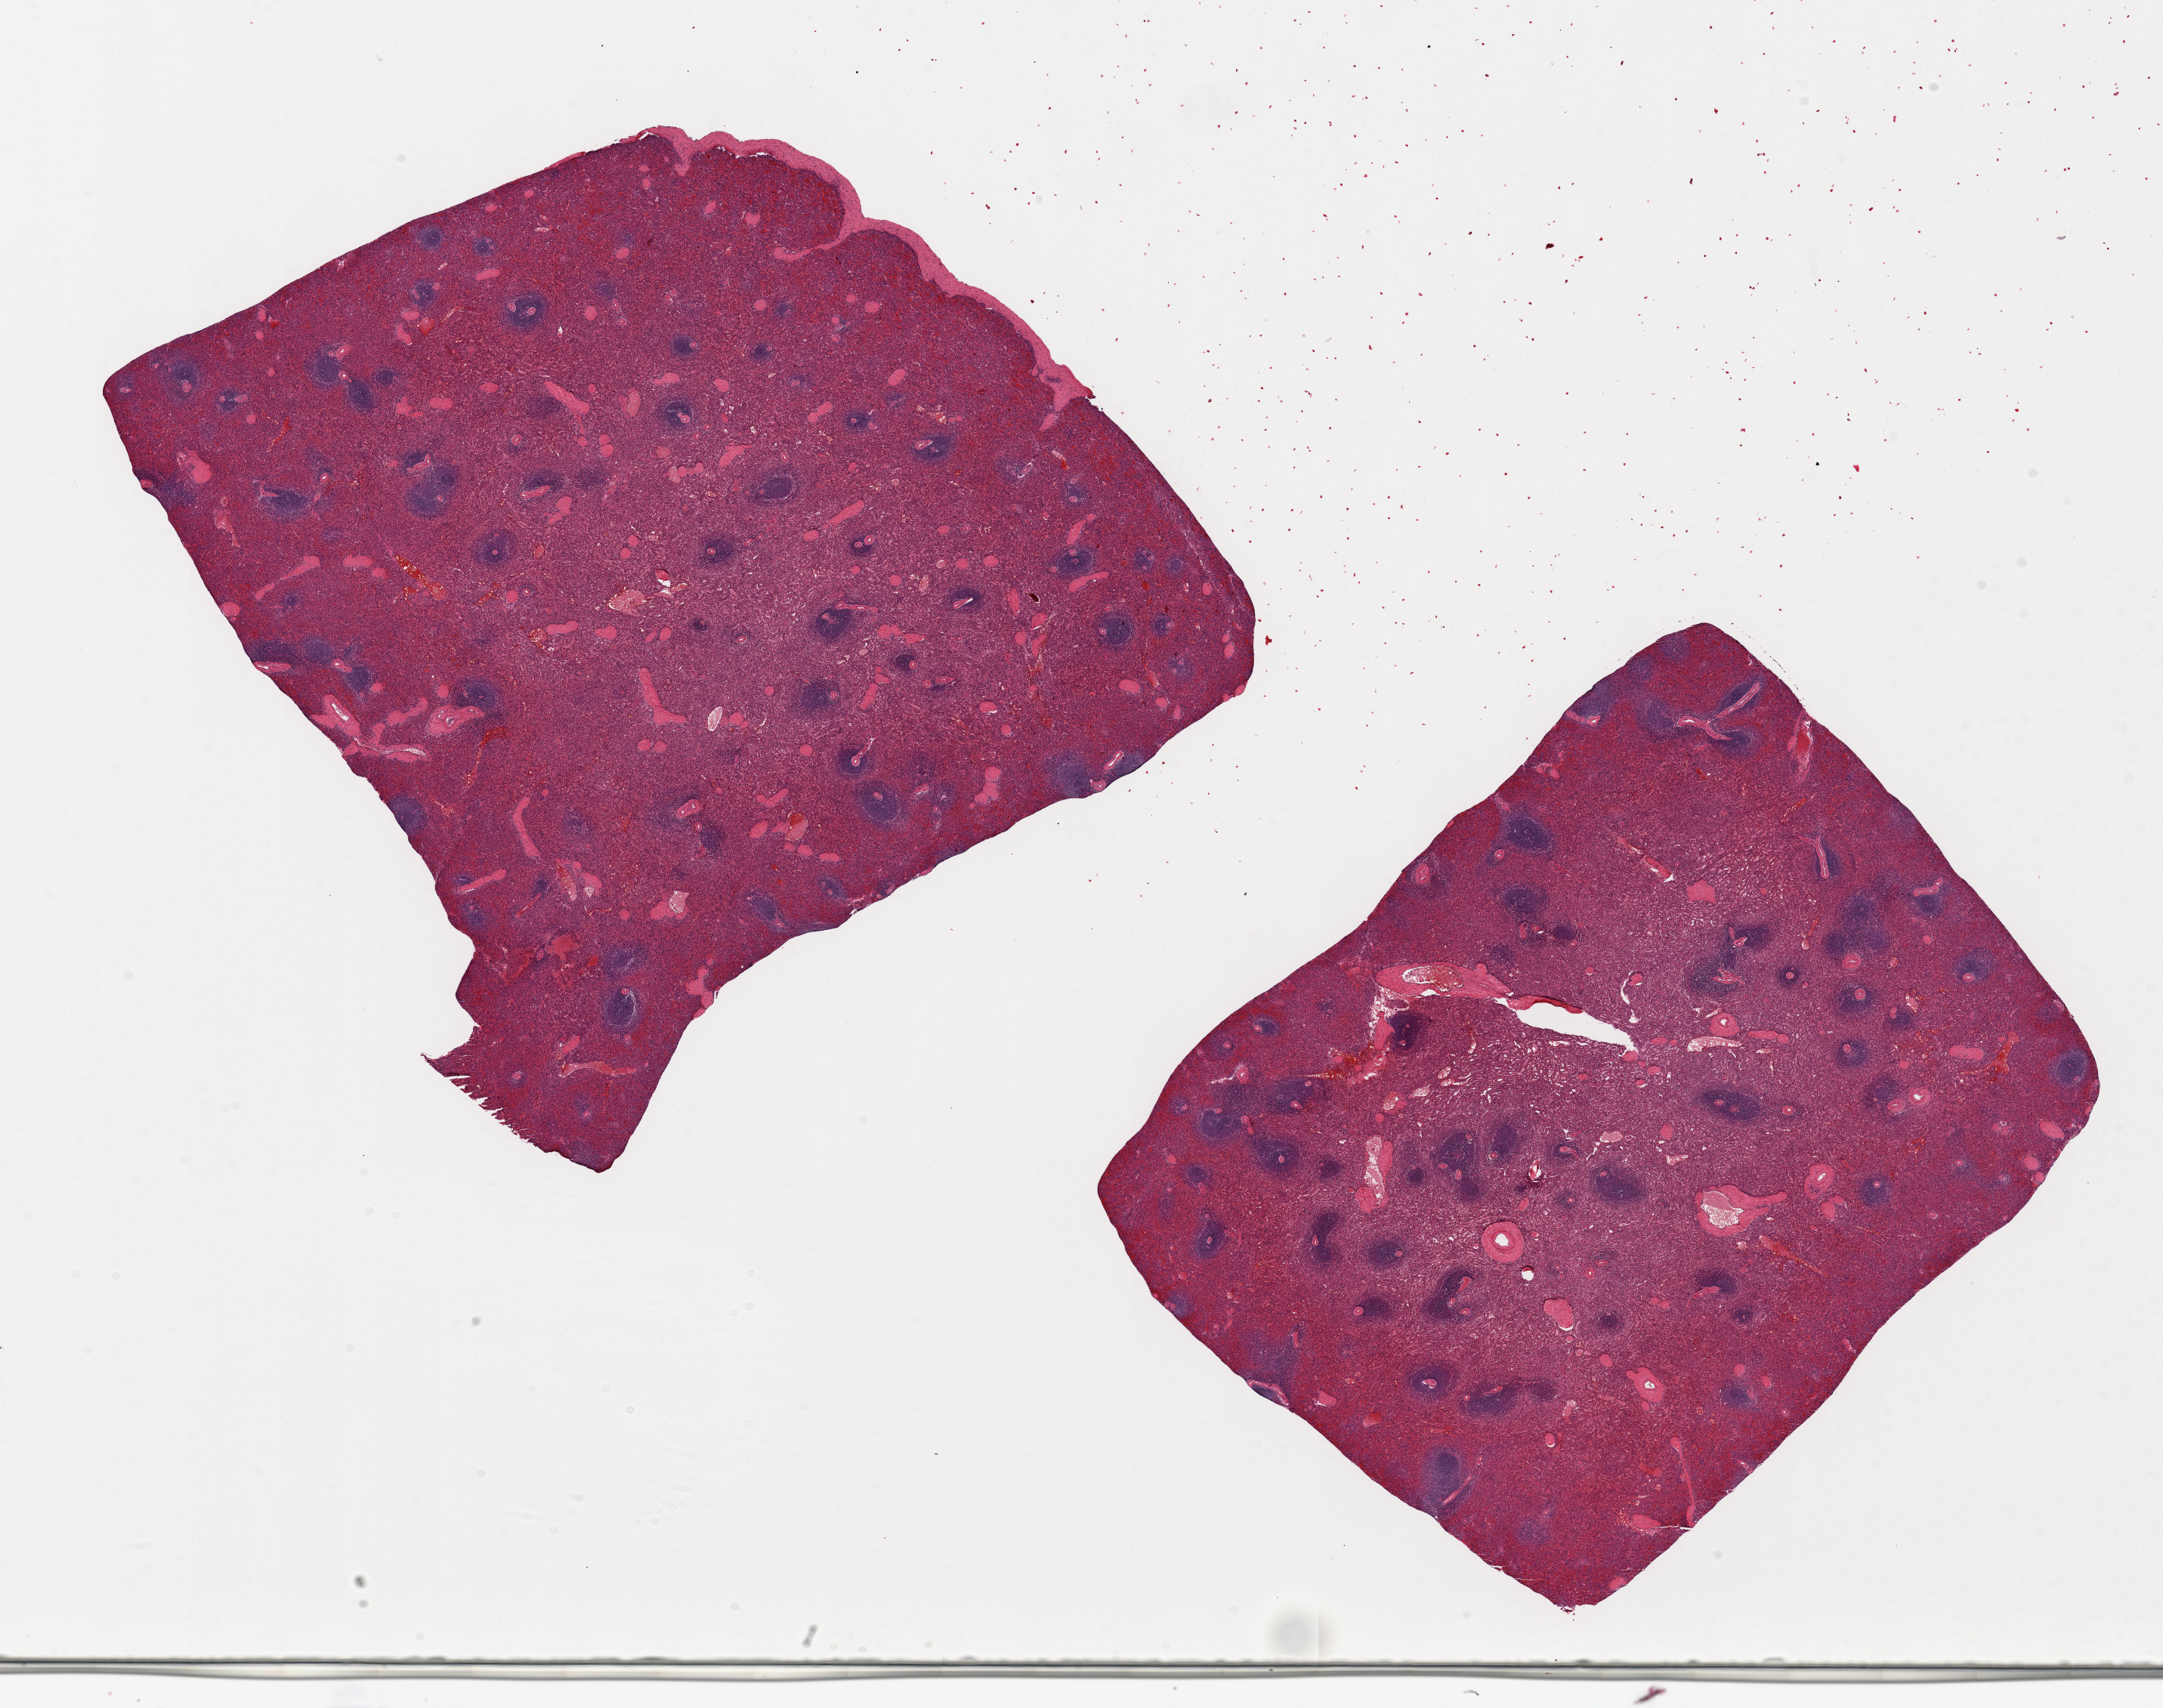
H&E whole-slide image — shown as a low-resolution overview of the whole scanned area (about 22.6 x 17.9 mm, from a 20x scan), PAXgene-fixed, paraffin-embedded tissue, sampled site (target tissue): spleen, donor tissue sample. Donor sex: female.
• reviewer comment on this tissue sample: 2 pieces, ~8x7mm